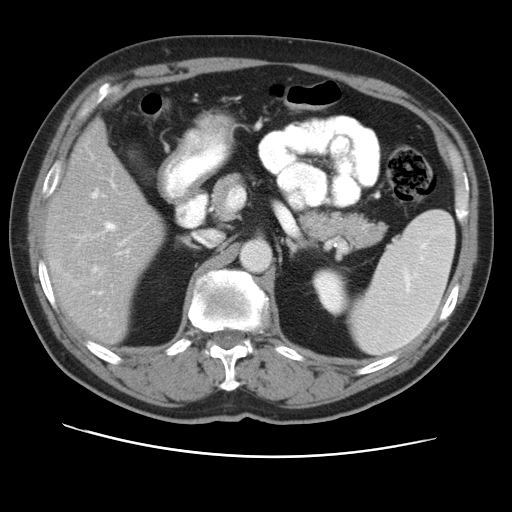
Contrast-enhanced abdominal CT, one axial slice; slice 25 of 49 in the series (ordered by position); reconstruction kernel STANDARD; soft-tissue window (W 400 / L 40 HU); 512 × 512 image matrix, field of view 374 × 374 mm. Male patient, age 59 years. Case-level facts recorded for this patient, not image findings: diagnosis: colorectal cancer liver metastases, imaged before liver resection; multiple liver metastases: yes.
Annotated regions visible in this slice (manually delineated by an expert):
- hepatic veins: bounding box (x1, y1, x2, y2) in pixels: (93, 190, 98, 197)
- liver: (46, 124, 163, 343)
- planned liver remnant (the part of the liver to remain after resection): (49, 124, 163, 343)
- portal vein (with intrahepatic branches): (93, 222, 129, 294)
- liver metastasis: (64, 262, 82, 279)